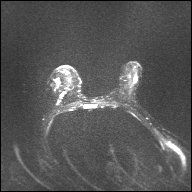
Breast MRI, one axial slice. Slice 22 of 32 in the series (ordered by position). Diffusion-weighted series; image 2 of 4 stored at this slice position (different b-values; order by instance number). 1.5 T. 192 × 192 image matrix, field of view 360 × 360 mm. Female patient.
Structures marked on this image (outlined manually by an expert reader):
- tumour on diffusion-weighted imaging: bounding box [x1, y1, x2, y2] px = [57, 81, 59, 84]